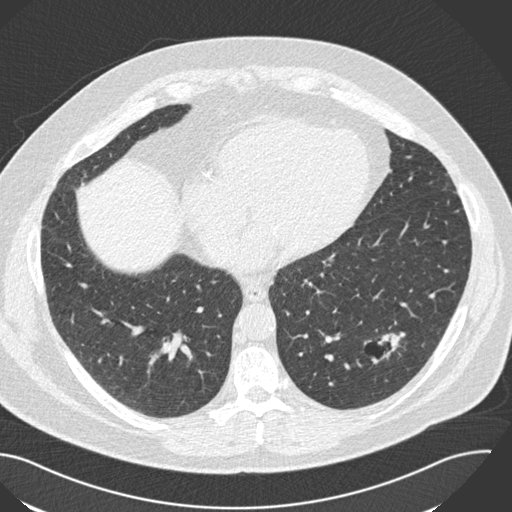
Low-dose screening chest CT, axial slice, third annual screen, lung window (W 1500 / L -600 HU), 512 × 512 image matrix, field of view 394 × 394 mm. Male participant, aged 57 years at enrolment. Current smoker at enrolment.
• Expert reader's lesion annotation, bounding box (x1, y1, x2, y2) in pixels: (349, 318, 423, 378).
• Reader record for this screening exam (exam-level; its link to the box is not recorded): non-calcified nodule or mass ≥4 mm, left lower lobe, 22 × 18 mm, poorly defined margins, soft tissue attenuation, pre-existing on the prior screen: yes; interval growth: yes.
• Lung cancer was diagnosed 124 days after this screen: squamous cell carcinoma, NOS, left lower lobe, moderately differentiated (G2), stage IA (AJCC 6th edition), 22 mm at pathology.